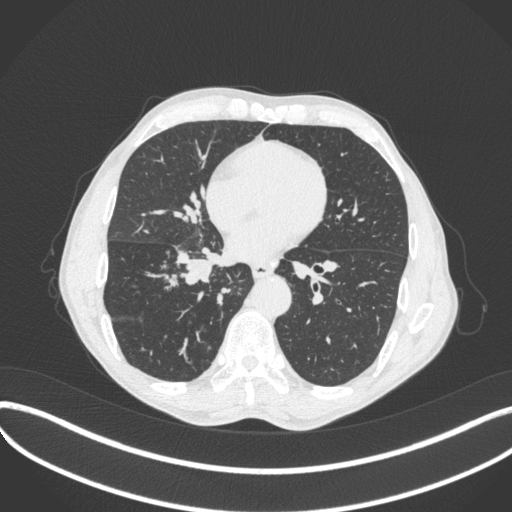
Chest CT, one axial slice. Slice 187 of 481 in the series (ordered by position). Reconstruction kernel B31f. Lung window (W 1500 / L -600 HU). 1 mm slice thickness. 512 × 512 image matrix, field of view 400 × 400 mm. Patient: male, 65 years. From the clinical record (not read from this slice): clinical TNM (as recorded): T2a N0 M0; histopathological grade: G2.
Structures marked on this image (rectangle marked by the reading radiologist):
- lung tumour (recorded histology: squamous cell carcinoma): bounding box <173,245,236,291> (left, top, right, bottom; pixels)